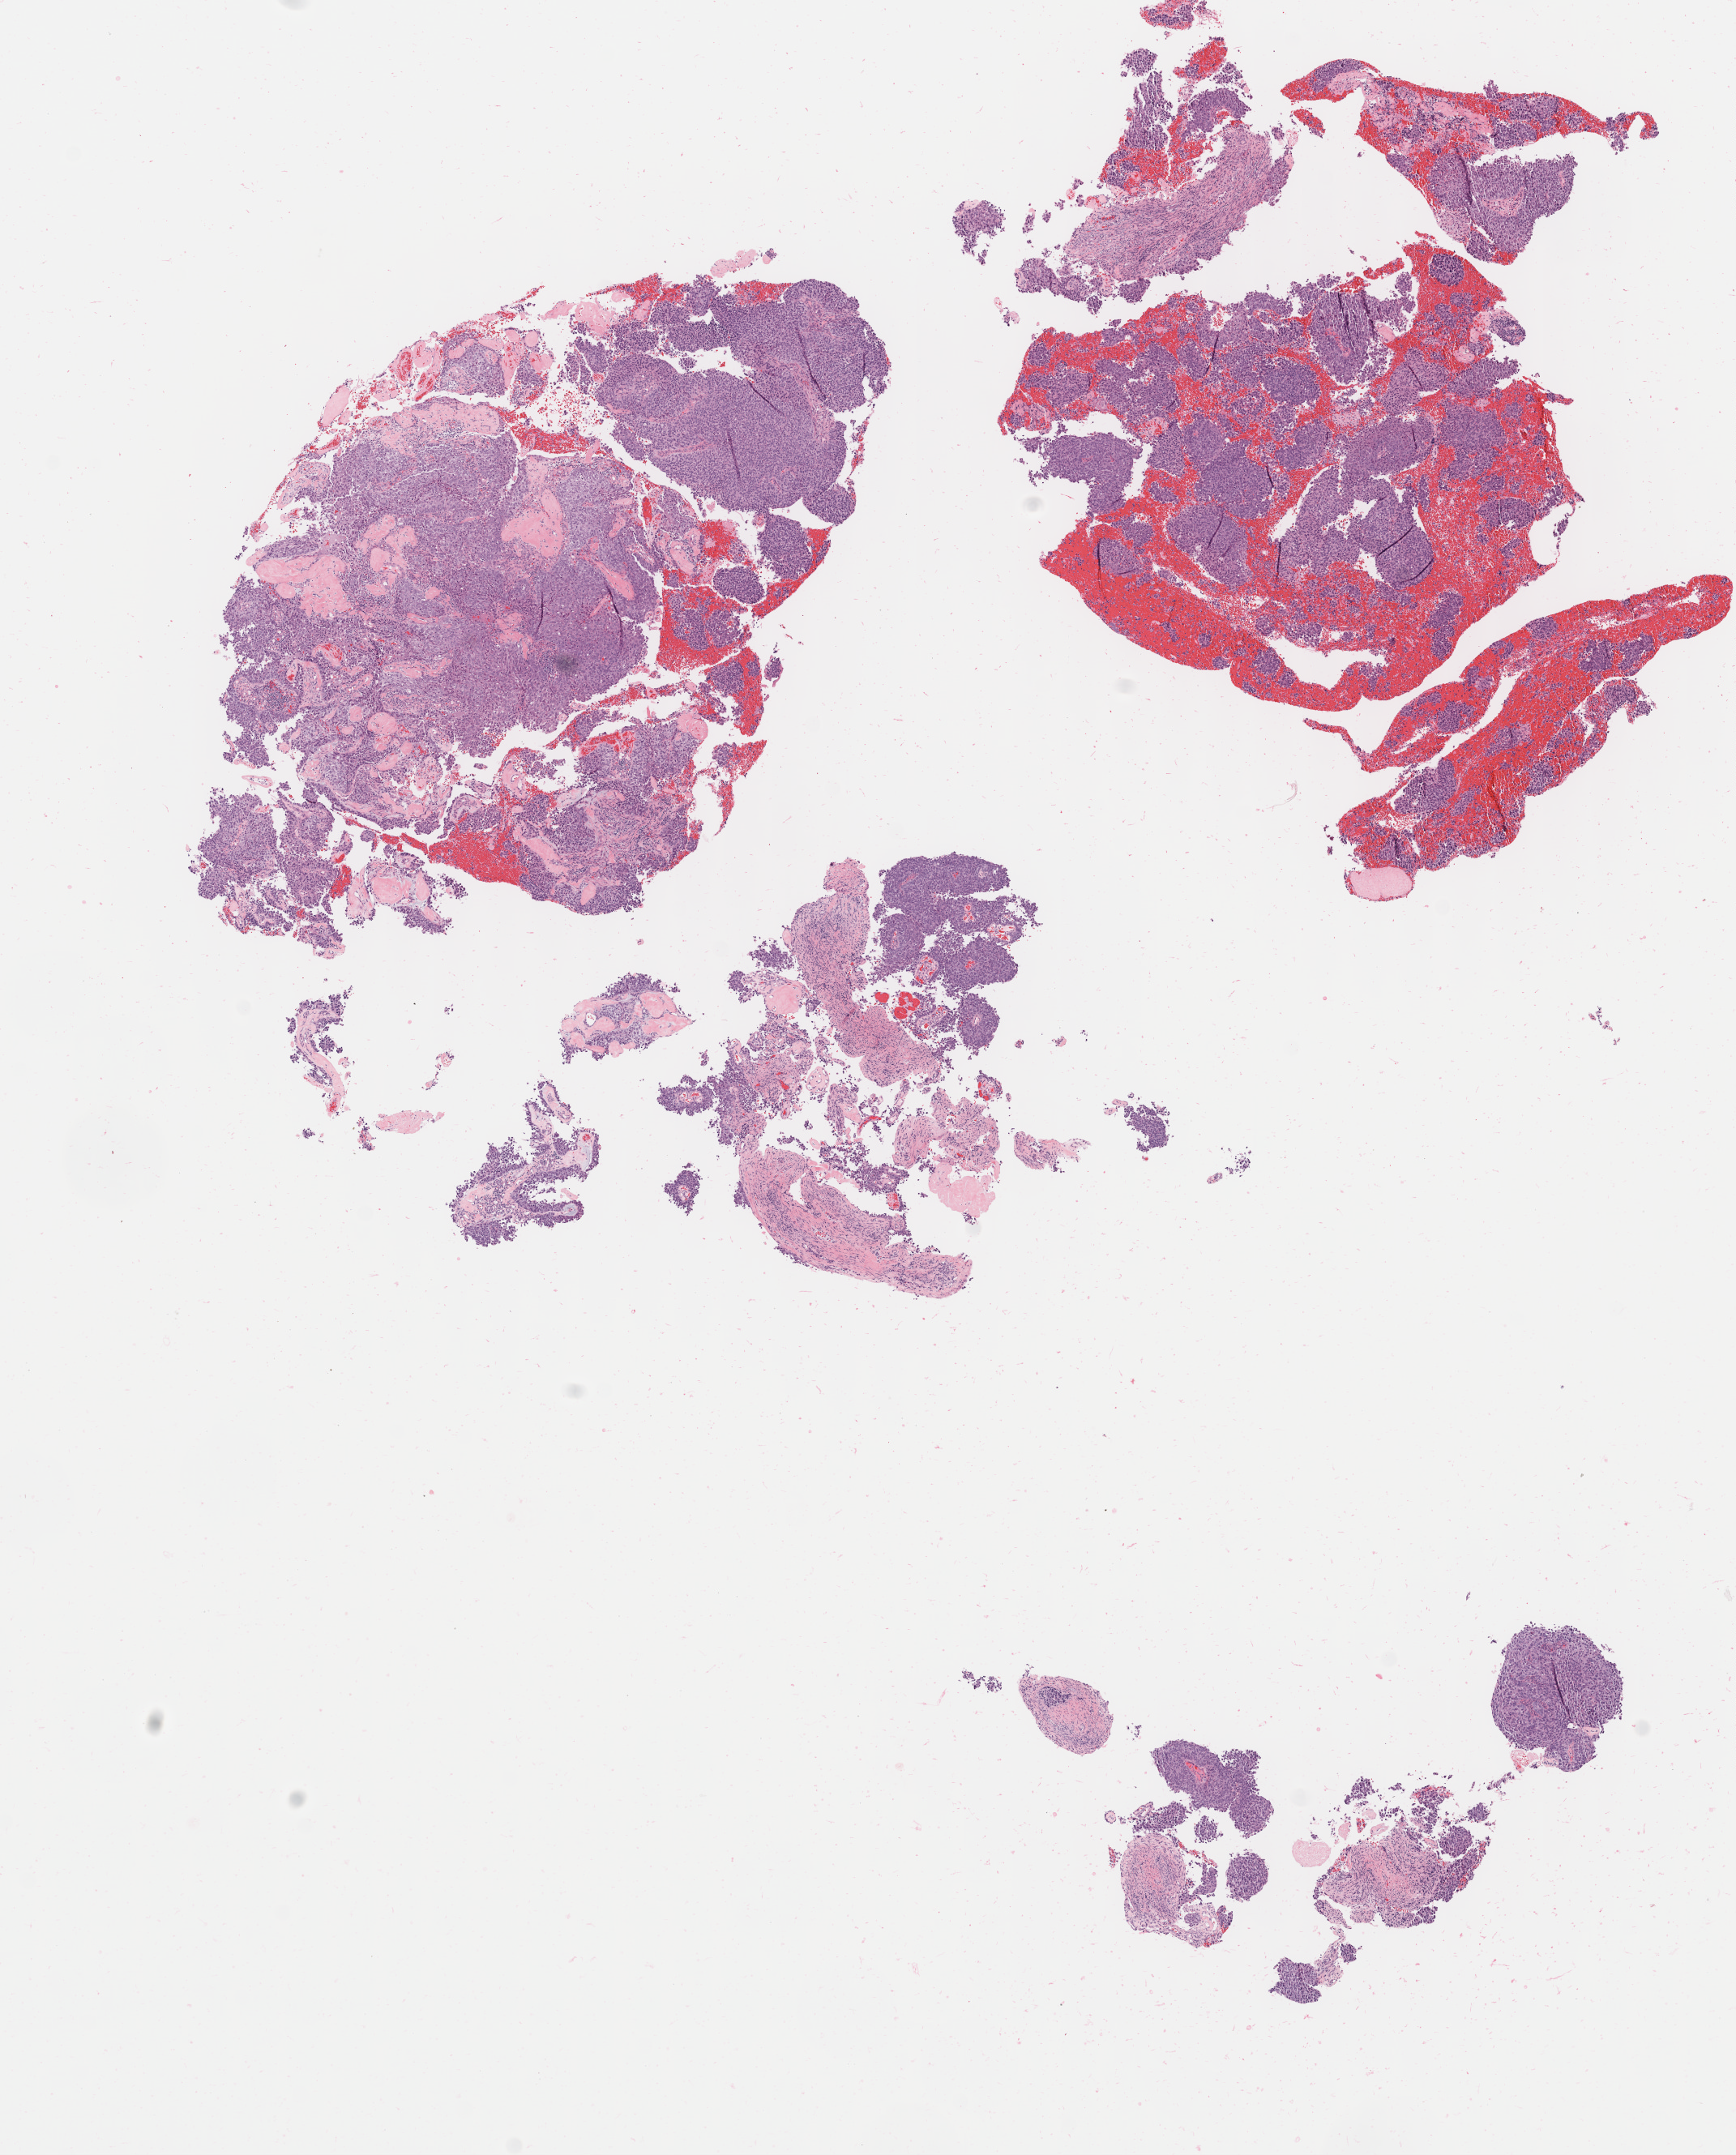
Digitized H&E-stained section, whole scanned area (about 8.5 x 10.6 mm) shown as a low-resolution overview; tumor tissue; site: cervix. Female patient, aged 44.
• diagnosis: Squamous cell carcinoma, large cell, nonkeratinizing, NOS